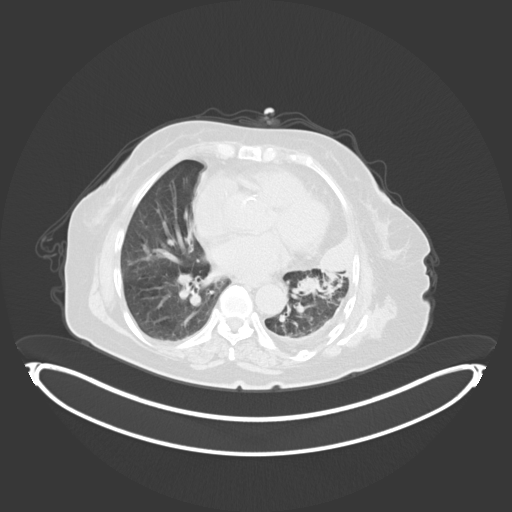
Chest CT, one axial slice; slice 190 of 284 in the series (ordered by position); reconstruction kernel B30f; 120 kVp; lung window (W 1500 / L -600 HU); 512 × 512 image matrix. Patient: female, 75 years. Case-level facts recorded for this patient, not image findings: clinical TNM (as recorded): T3 N3 M1.
Structures marked on this image (bounding box drawn by a radiologist):
- lung tumour (recorded histology: adenocarcinoma): box from (x=314, y=228) to (x=359, y=280) px